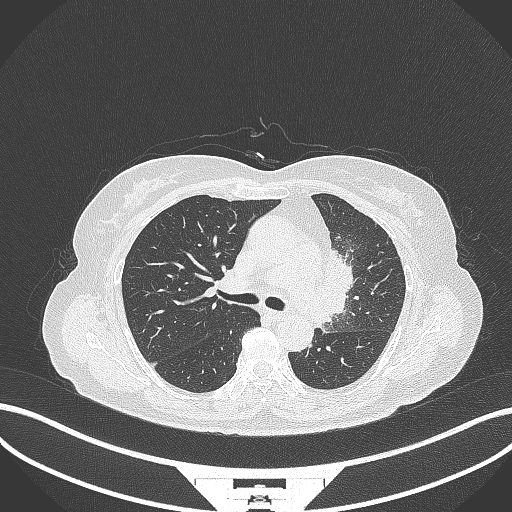
Chest CT, one axial slice; slice 211 of 382 in the series (ordered by position); 120 kVp; lung window (W 1500 / L -600 HU); 1 mm slice thickness; 512 × 512 image matrix. Female patient, age 64 years. From the clinical record (not read from this slice): clinical TNM (as recorded): T2a N2 M0.
Outlined on this slice (bounding box drawn by a radiologist):
- lung tumour (recorded histology: adenocarcinoma): bounding box [x1, y1, x2, y2] px = [317, 243, 358, 318]